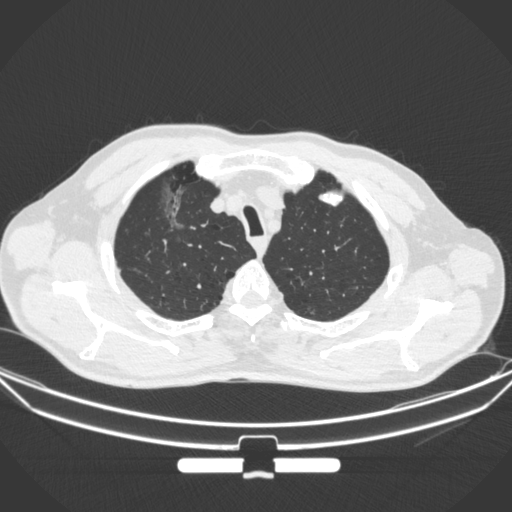
Chest CT, one axial slice. Position 292 of 355 along the scan axis. 120 kVp. Lung window (W 1500 / L -600 HU). 1 mm slice thickness. 512 × 512 image matrix. Male patient, age 67 years. From the clinical record (not read from this slice): clinical TNM (as recorded): T1c N0 M0.
Outlined on this slice (bounding box drawn by a radiologist):
- lung tumour (recorded histology: adenocarcinoma): bounding box <152,177,190,230> (left, top, right, bottom; pixels)